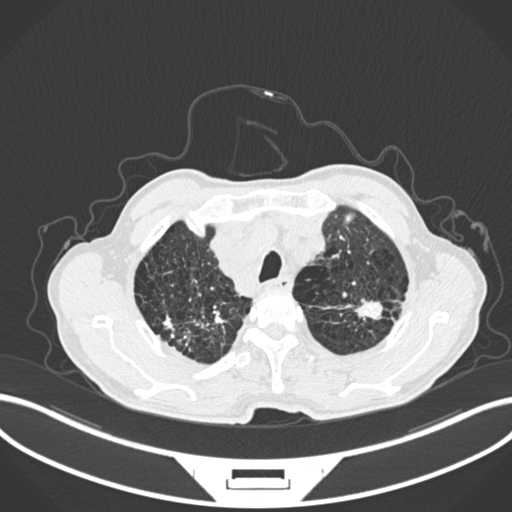
Chest CT, one axial slice. 120 kVp. Lung window (W 1500 / L -600 HU). 1 mm slice thickness. 512 × 512 image matrix, field of view 400 × 400 mm. Patient: male, 74 years. From the clinical record (not read from this slice): clinical TNM (as recorded): T2a N1 M0.
Annotated regions visible in this slice (rectangle marked by the reading radiologist):
- lung tumour (recorded histology: adenocarcinoma): bounding box [x1, y1, x2, y2] px = [351, 297, 388, 324]